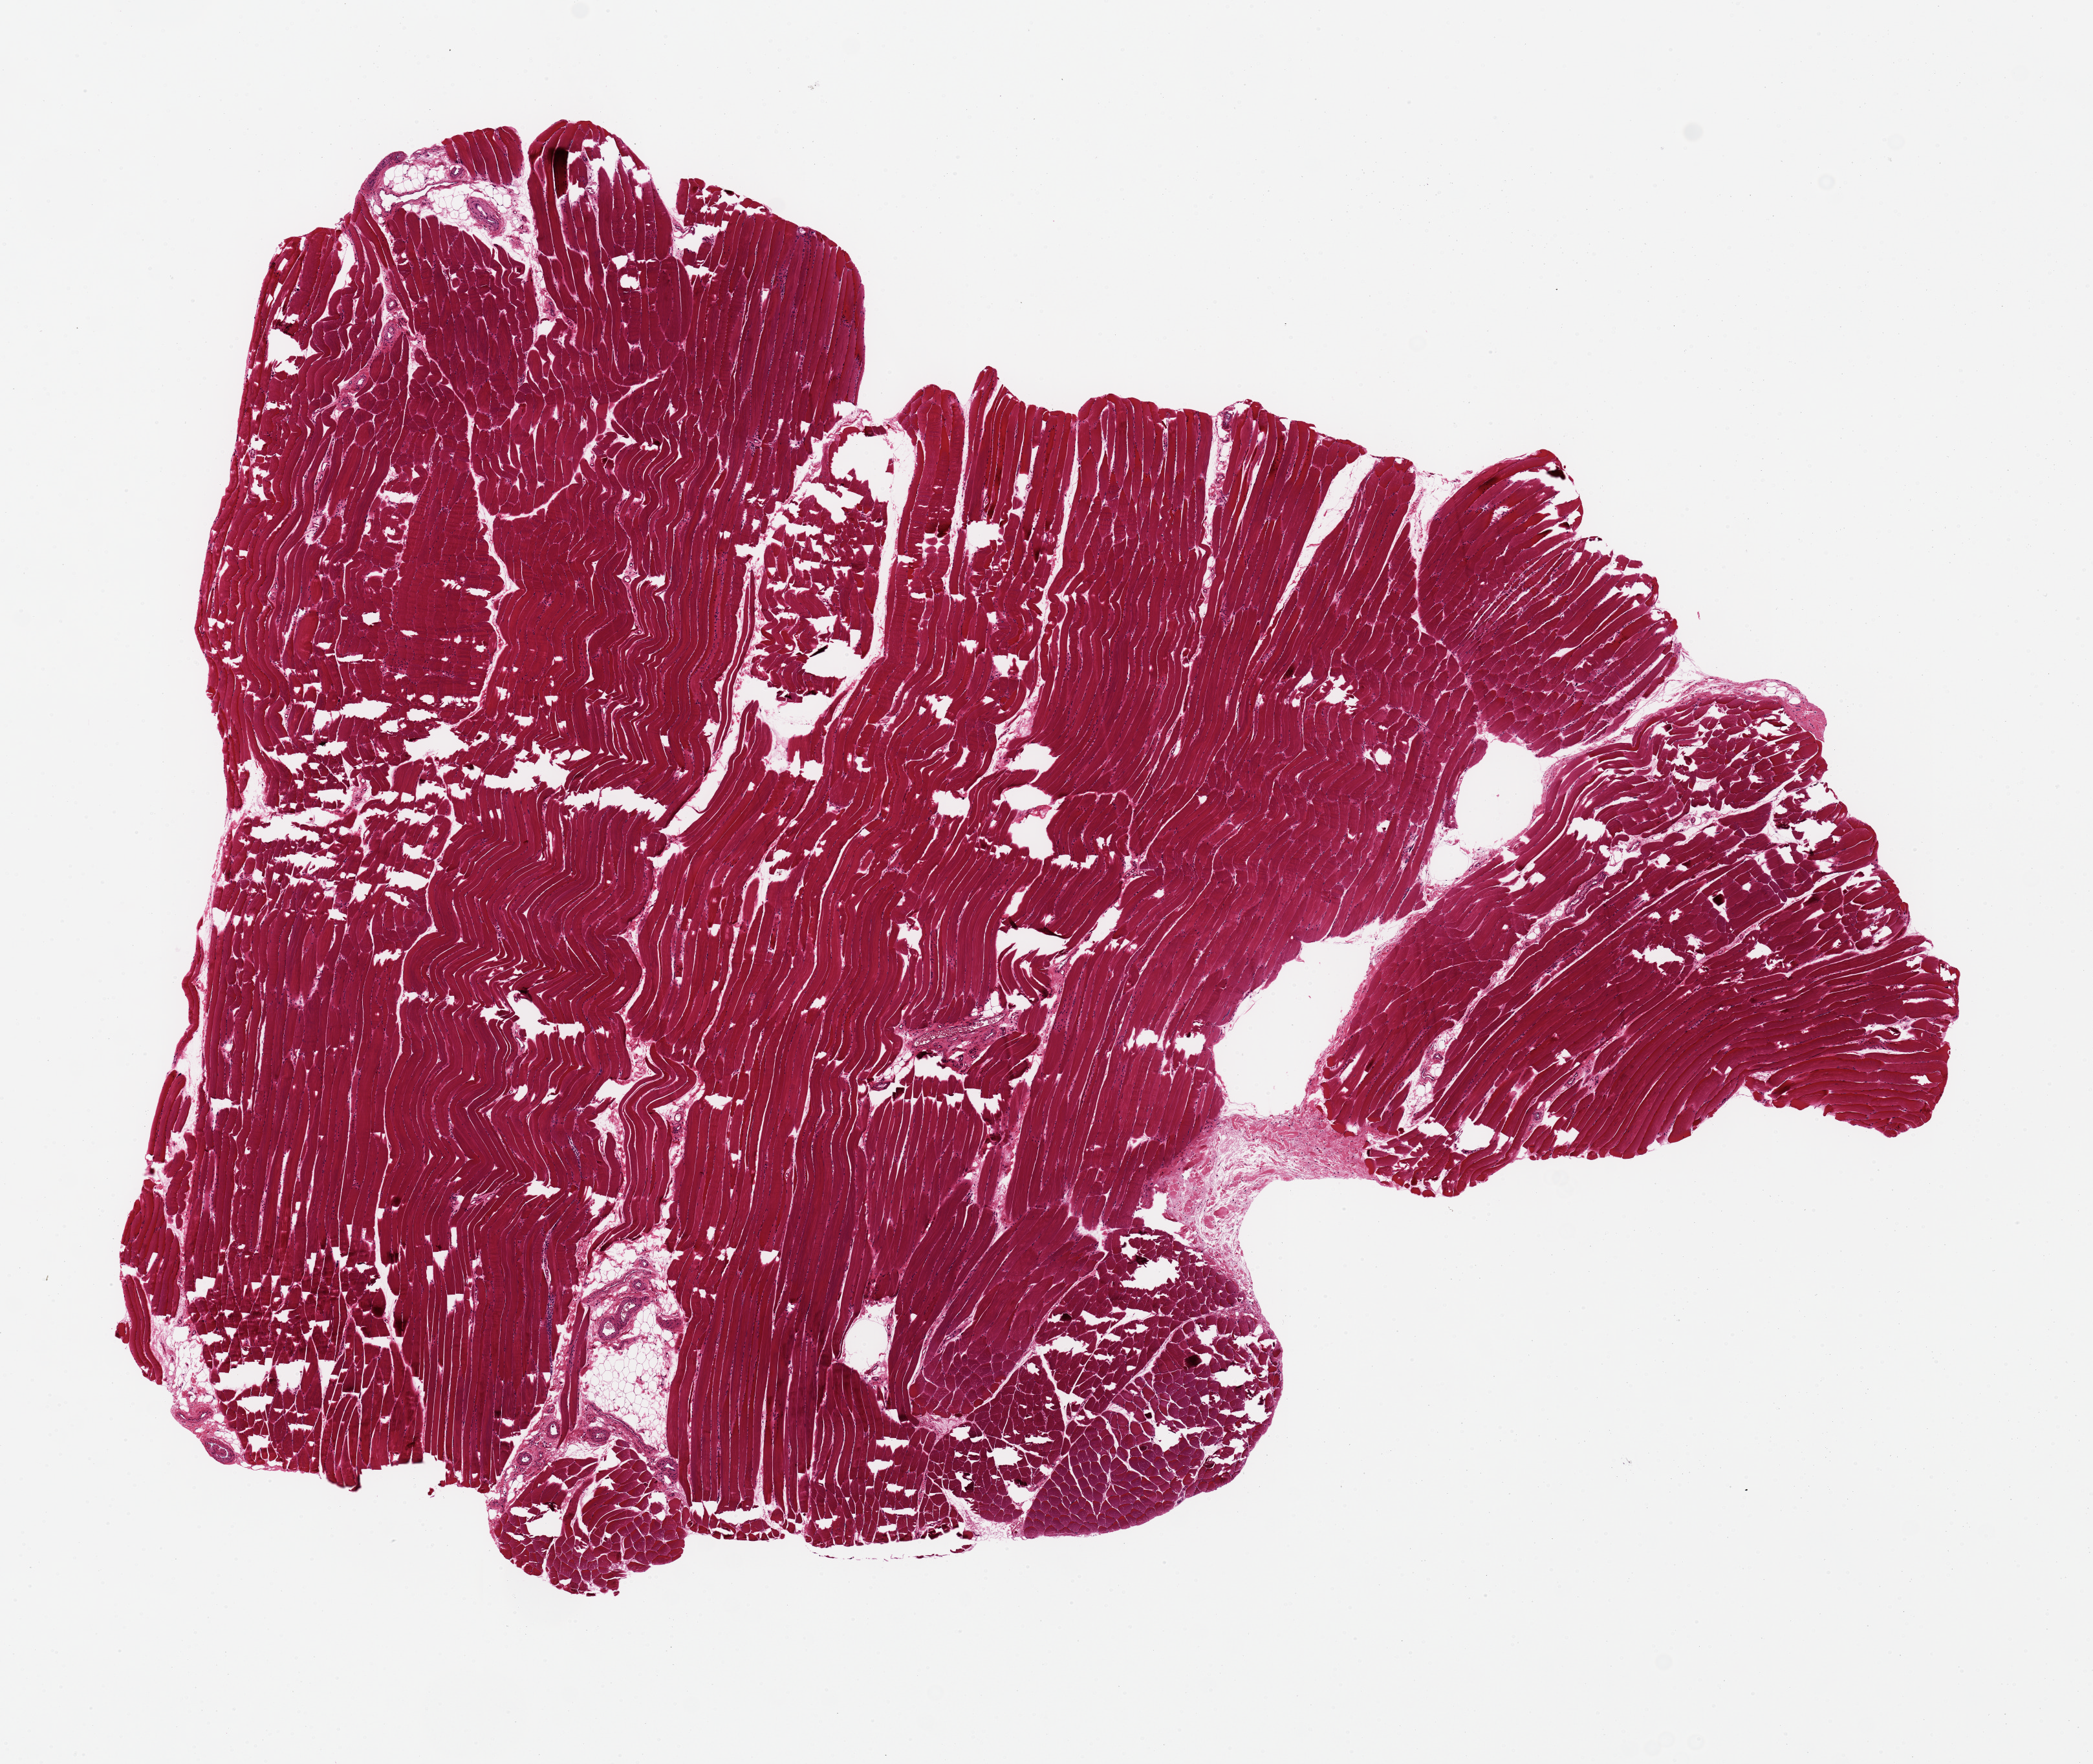
Digitized H&E-stained section, a low-resolution overview of the entire scanned area, about 12.8 x 10.8 mm, PAXgene-fixed paraffin-embedded (PFPE) section, section of skeletal muscle (target tissue), donor tissue sample.
* pathologist's review note for this sample: less than 1% intermingled adipose tissue